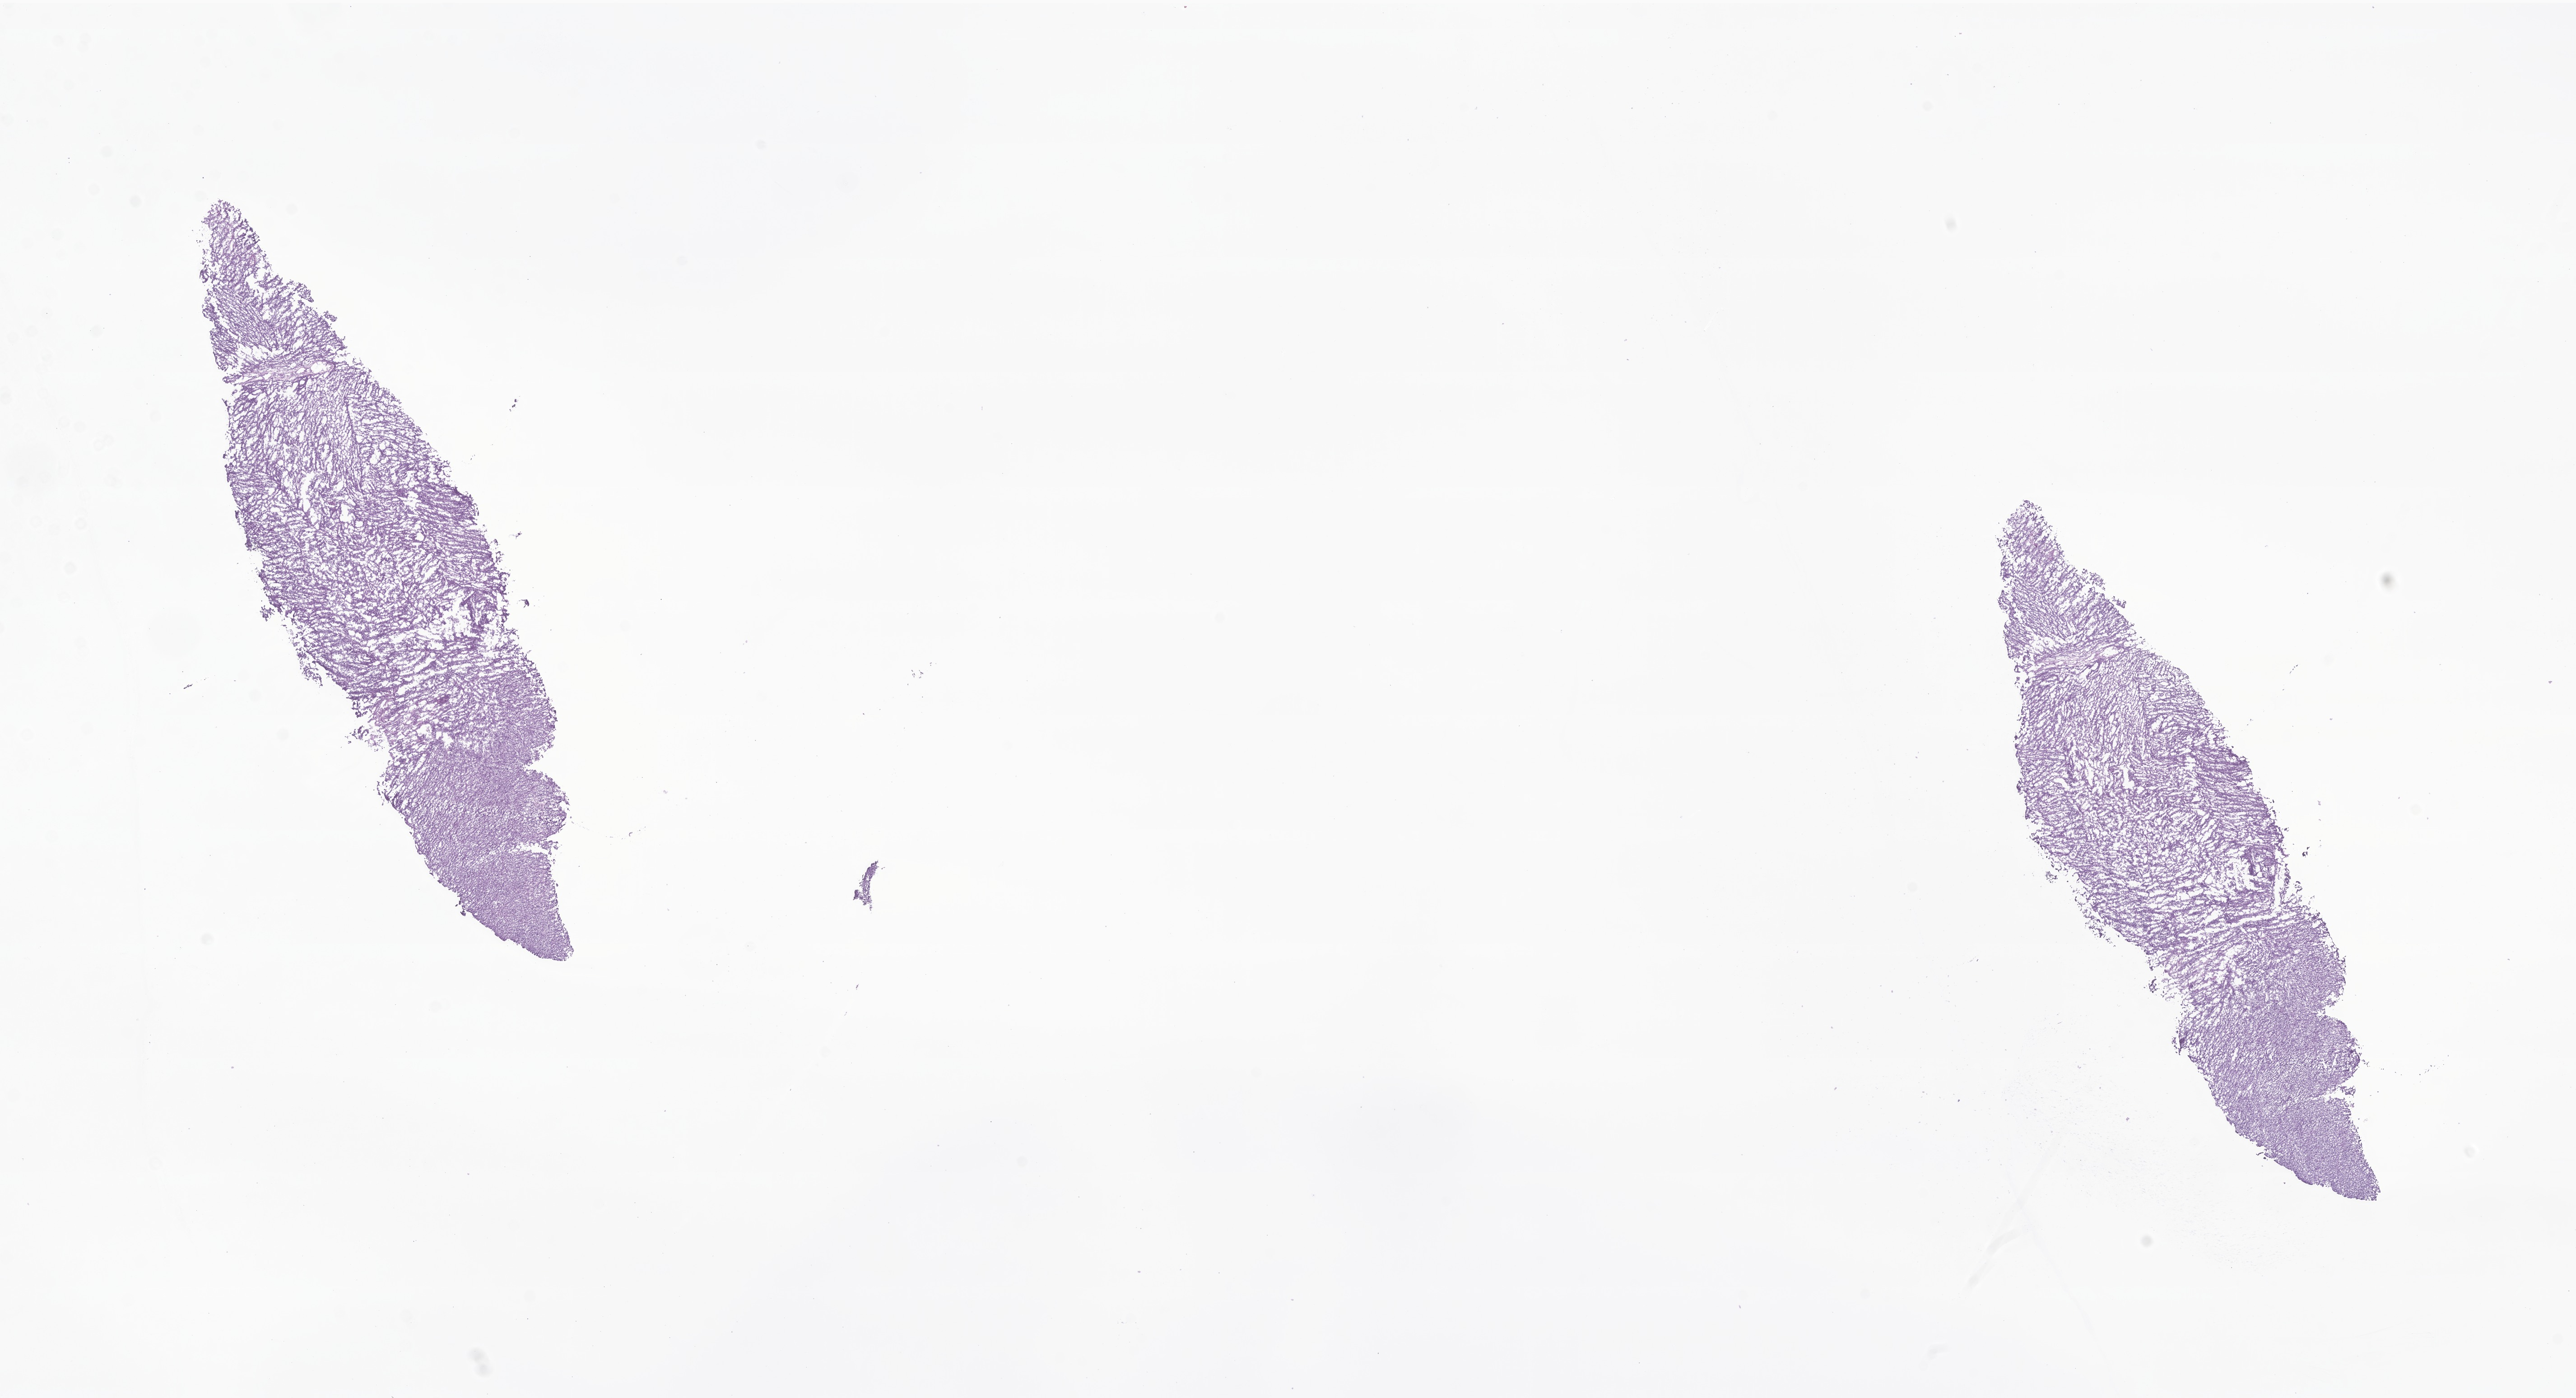
Hematoxylin and eosin (H&E) whole-slide image of tumor tissue from the brain — low-resolution overview of the scanned area, about 24.1 x 13.1 mm, frozen section (OCT-embedded). Male patient, age 69 months (5 years 9 months).
Diagnosis: Glioma, malignant.